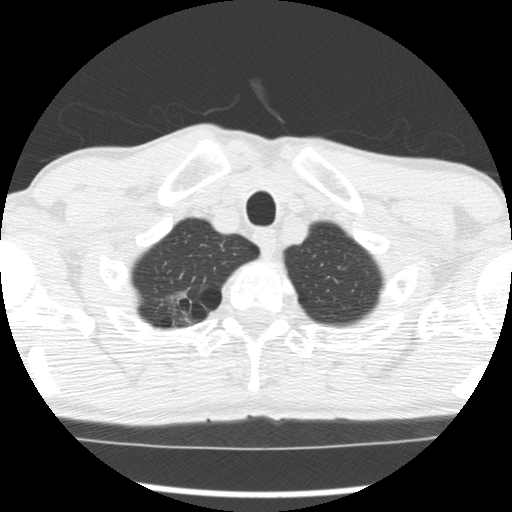
Low-dose screening chest CT, axial slice, first (baseline) screen, lung window (W 1500 / L -600 HU), slice 21 of 277 in the series, 512 × 512 image matrix. Male participant, aged 66 years at enrolment.
- Expert reader's lesion annotation, bounding box (x1, y1, x2, y2) in pixels: (147, 284, 206, 335).
- The screening reader recorded 4 non-calcified nodules or masses ≥4 mm on this exam (right upper lobe, right upper lobe, right upper lobe, left lower lobe); which of them this box marks is not recorded.
- Official screen result: positive, change unspecified: nodule(s) >= 4 mm or enlarging nodule(s), mass(es), or other non-specific abnormalities suspicious for lung cancer.
- Lung cancer was diagnosed 503 days after this screen: adenocarcinoma, NOS, right upper lobe, undifferentiated (G4), stage IA (AJCC 6th edition), 20 mm at pathology.